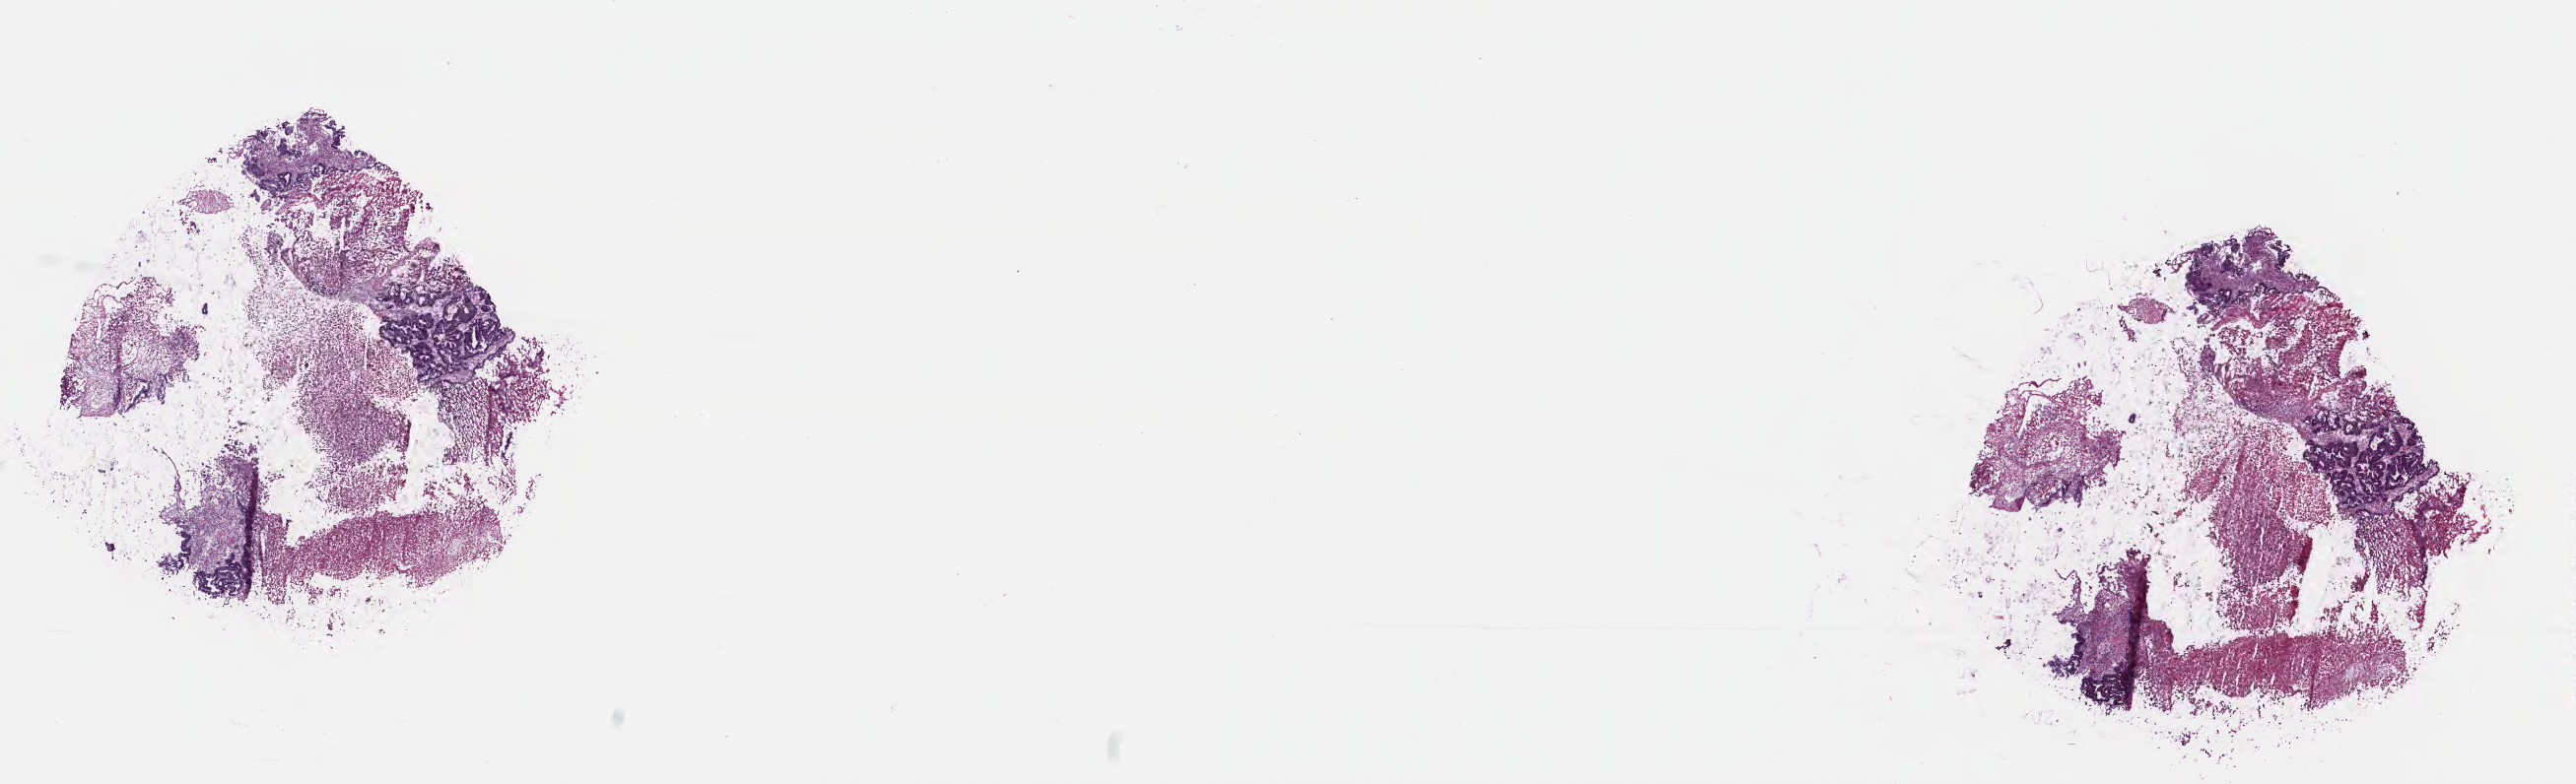
Digitized haematoxylin and eosin-stained section — whole scanned area (about 21.1 x 6.4 mm) shown as a low-resolution overview; cryosection; metastatic tumor tissue, resected from pelvis. Female patient; age at initial diagnosis 66 years. Pathologist review of this section (percent, as recorded): tumor cells 40%, tumor nuclei 50%, stromal cells 35%, necrosis 10%, normal cells 15%. Inflammatory infiltration, as recorded: lymphocyte infiltration 5%, monocyte infiltration 2%, neutrophil infiltration 5%.
Patient diagnosis (primary): Adenocarcinoma, metastatic, NOS.